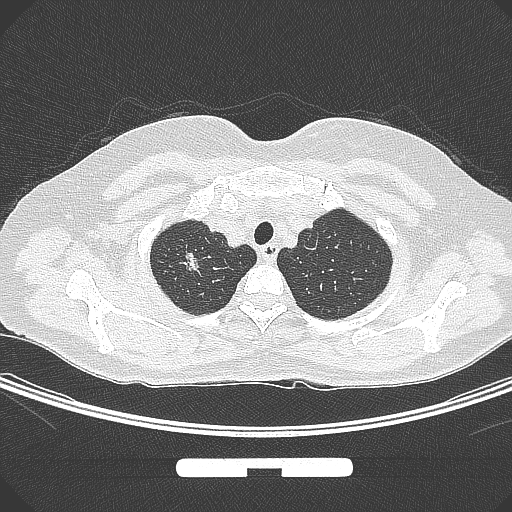
Chest CT, one axial slice; position 258 of 295 along the scan axis; 120 kVp; lung window (W 1500 / L -600 HU); 1 mm slice thickness; 512 × 512 image matrix, field of view 369 × 369 mm. Female patient, age 58 years. Case-level facts recorded for this patient, not image findings: clinical TNM (as recorded): T1b N0 M0; histopathological grade: G2-3.
Outlined on this slice (bounding box drawn by a radiologist):
- lung tumour (recorded histology: adenocarcinoma): bounding box <172,243,201,290> (left, top, right, bottom; pixels)